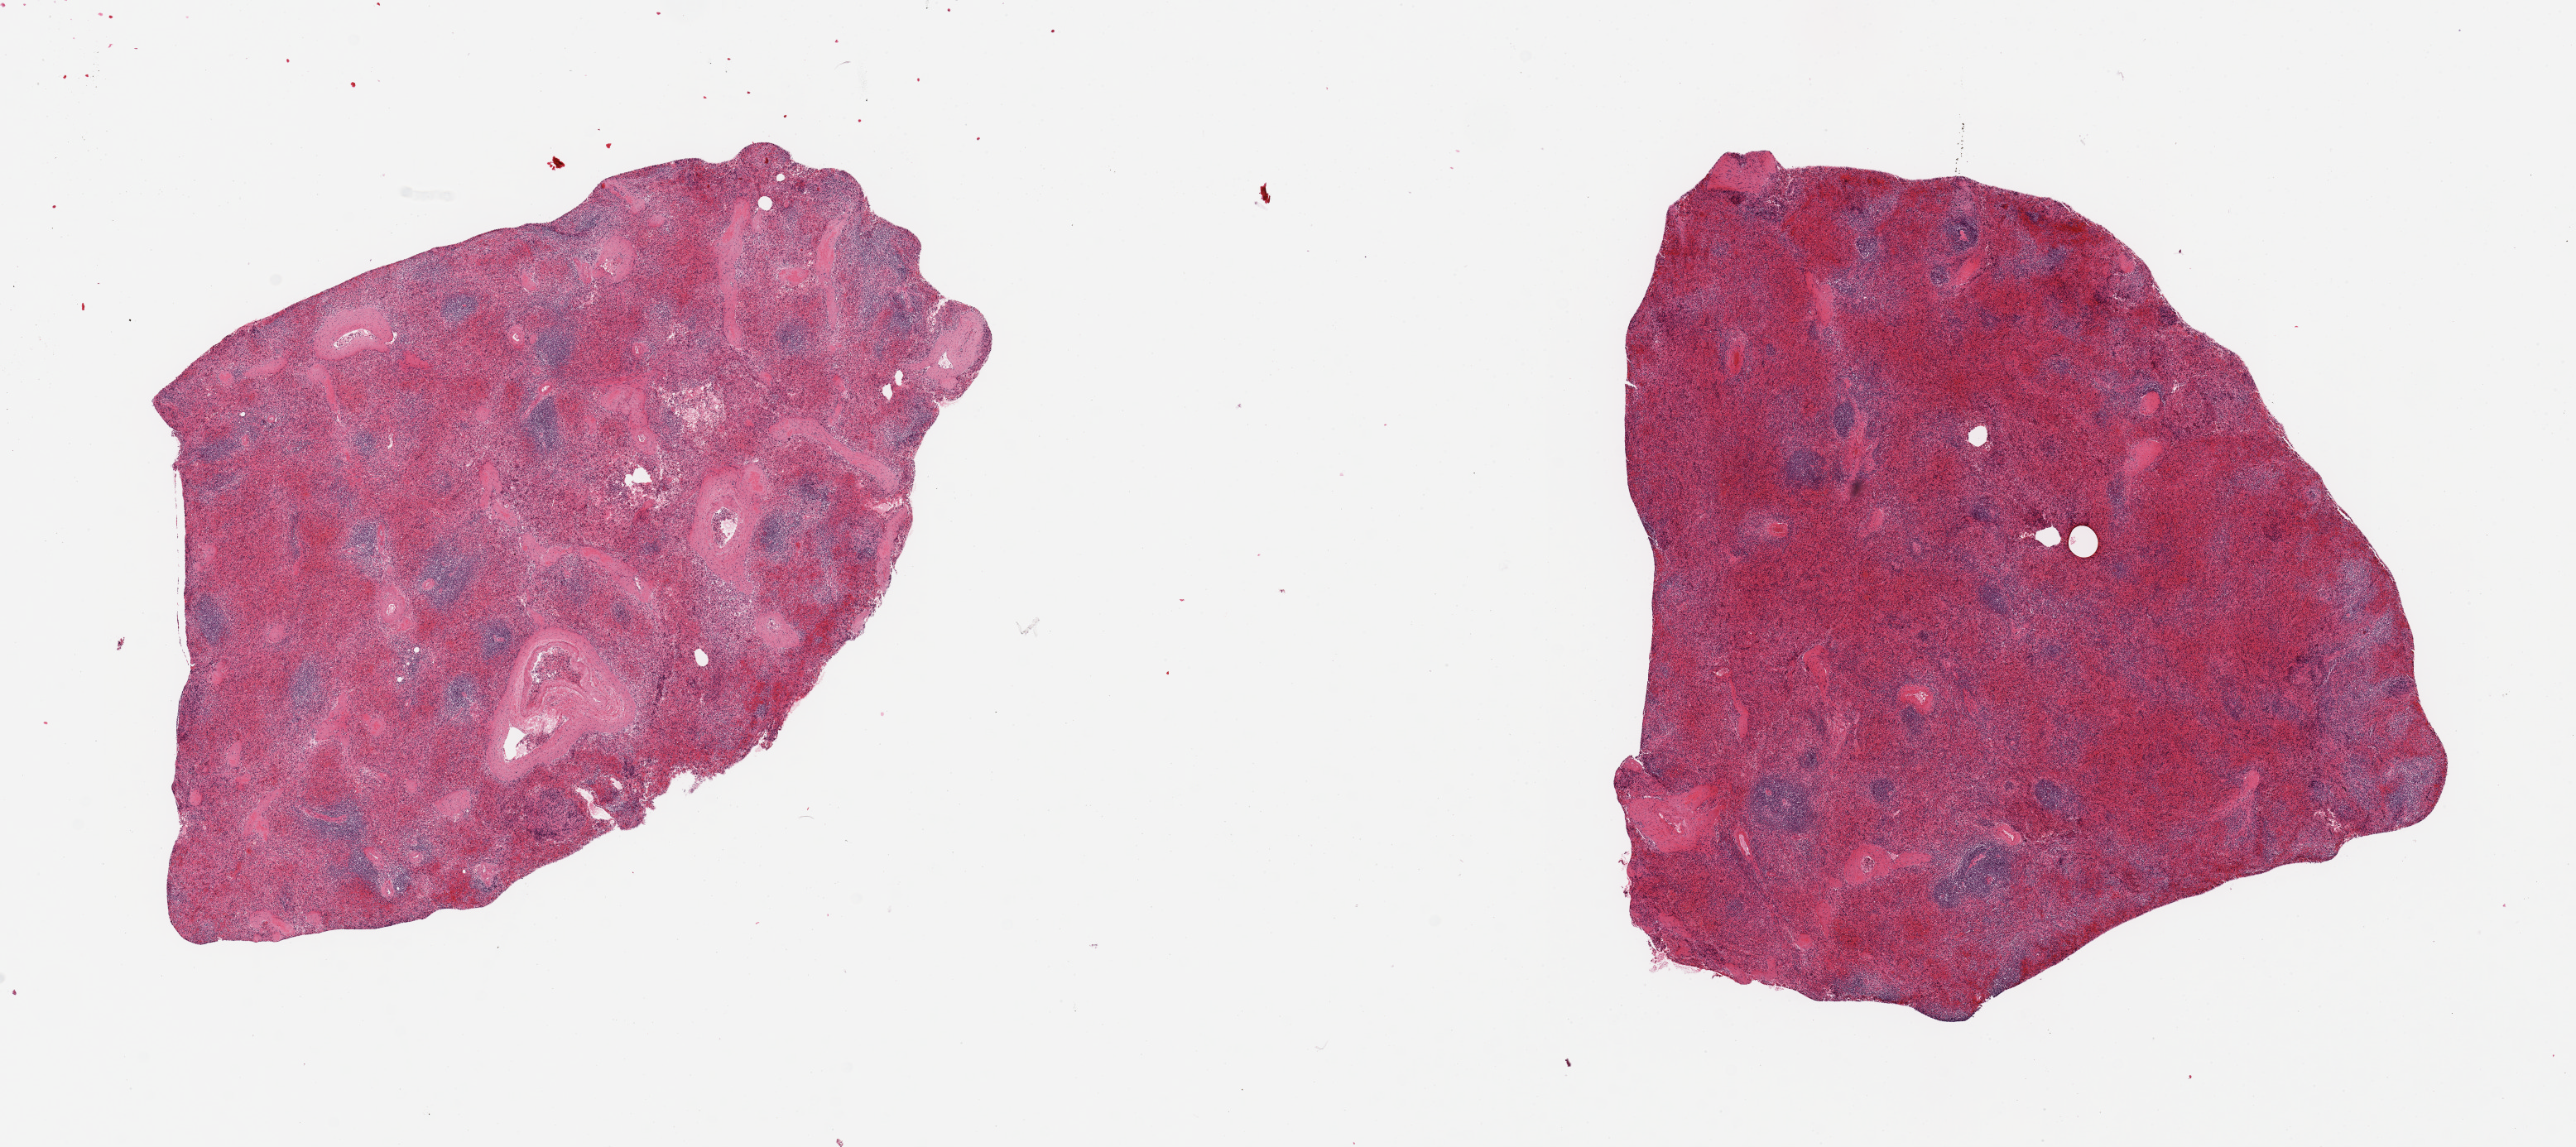
Whole-slide image, H&E stain, brightfield, a low-resolution overview of the entire scanned area, about 24.6 x 11.0 mm (from a 20x scan). PAXgene-fixed, paraffin-embedded tissue. Sampled site (target tissue): spleen. Donor tissue sample. Donor sex: female.
Review note (as recorded): 2 pieces, congestion, marked autolysis.